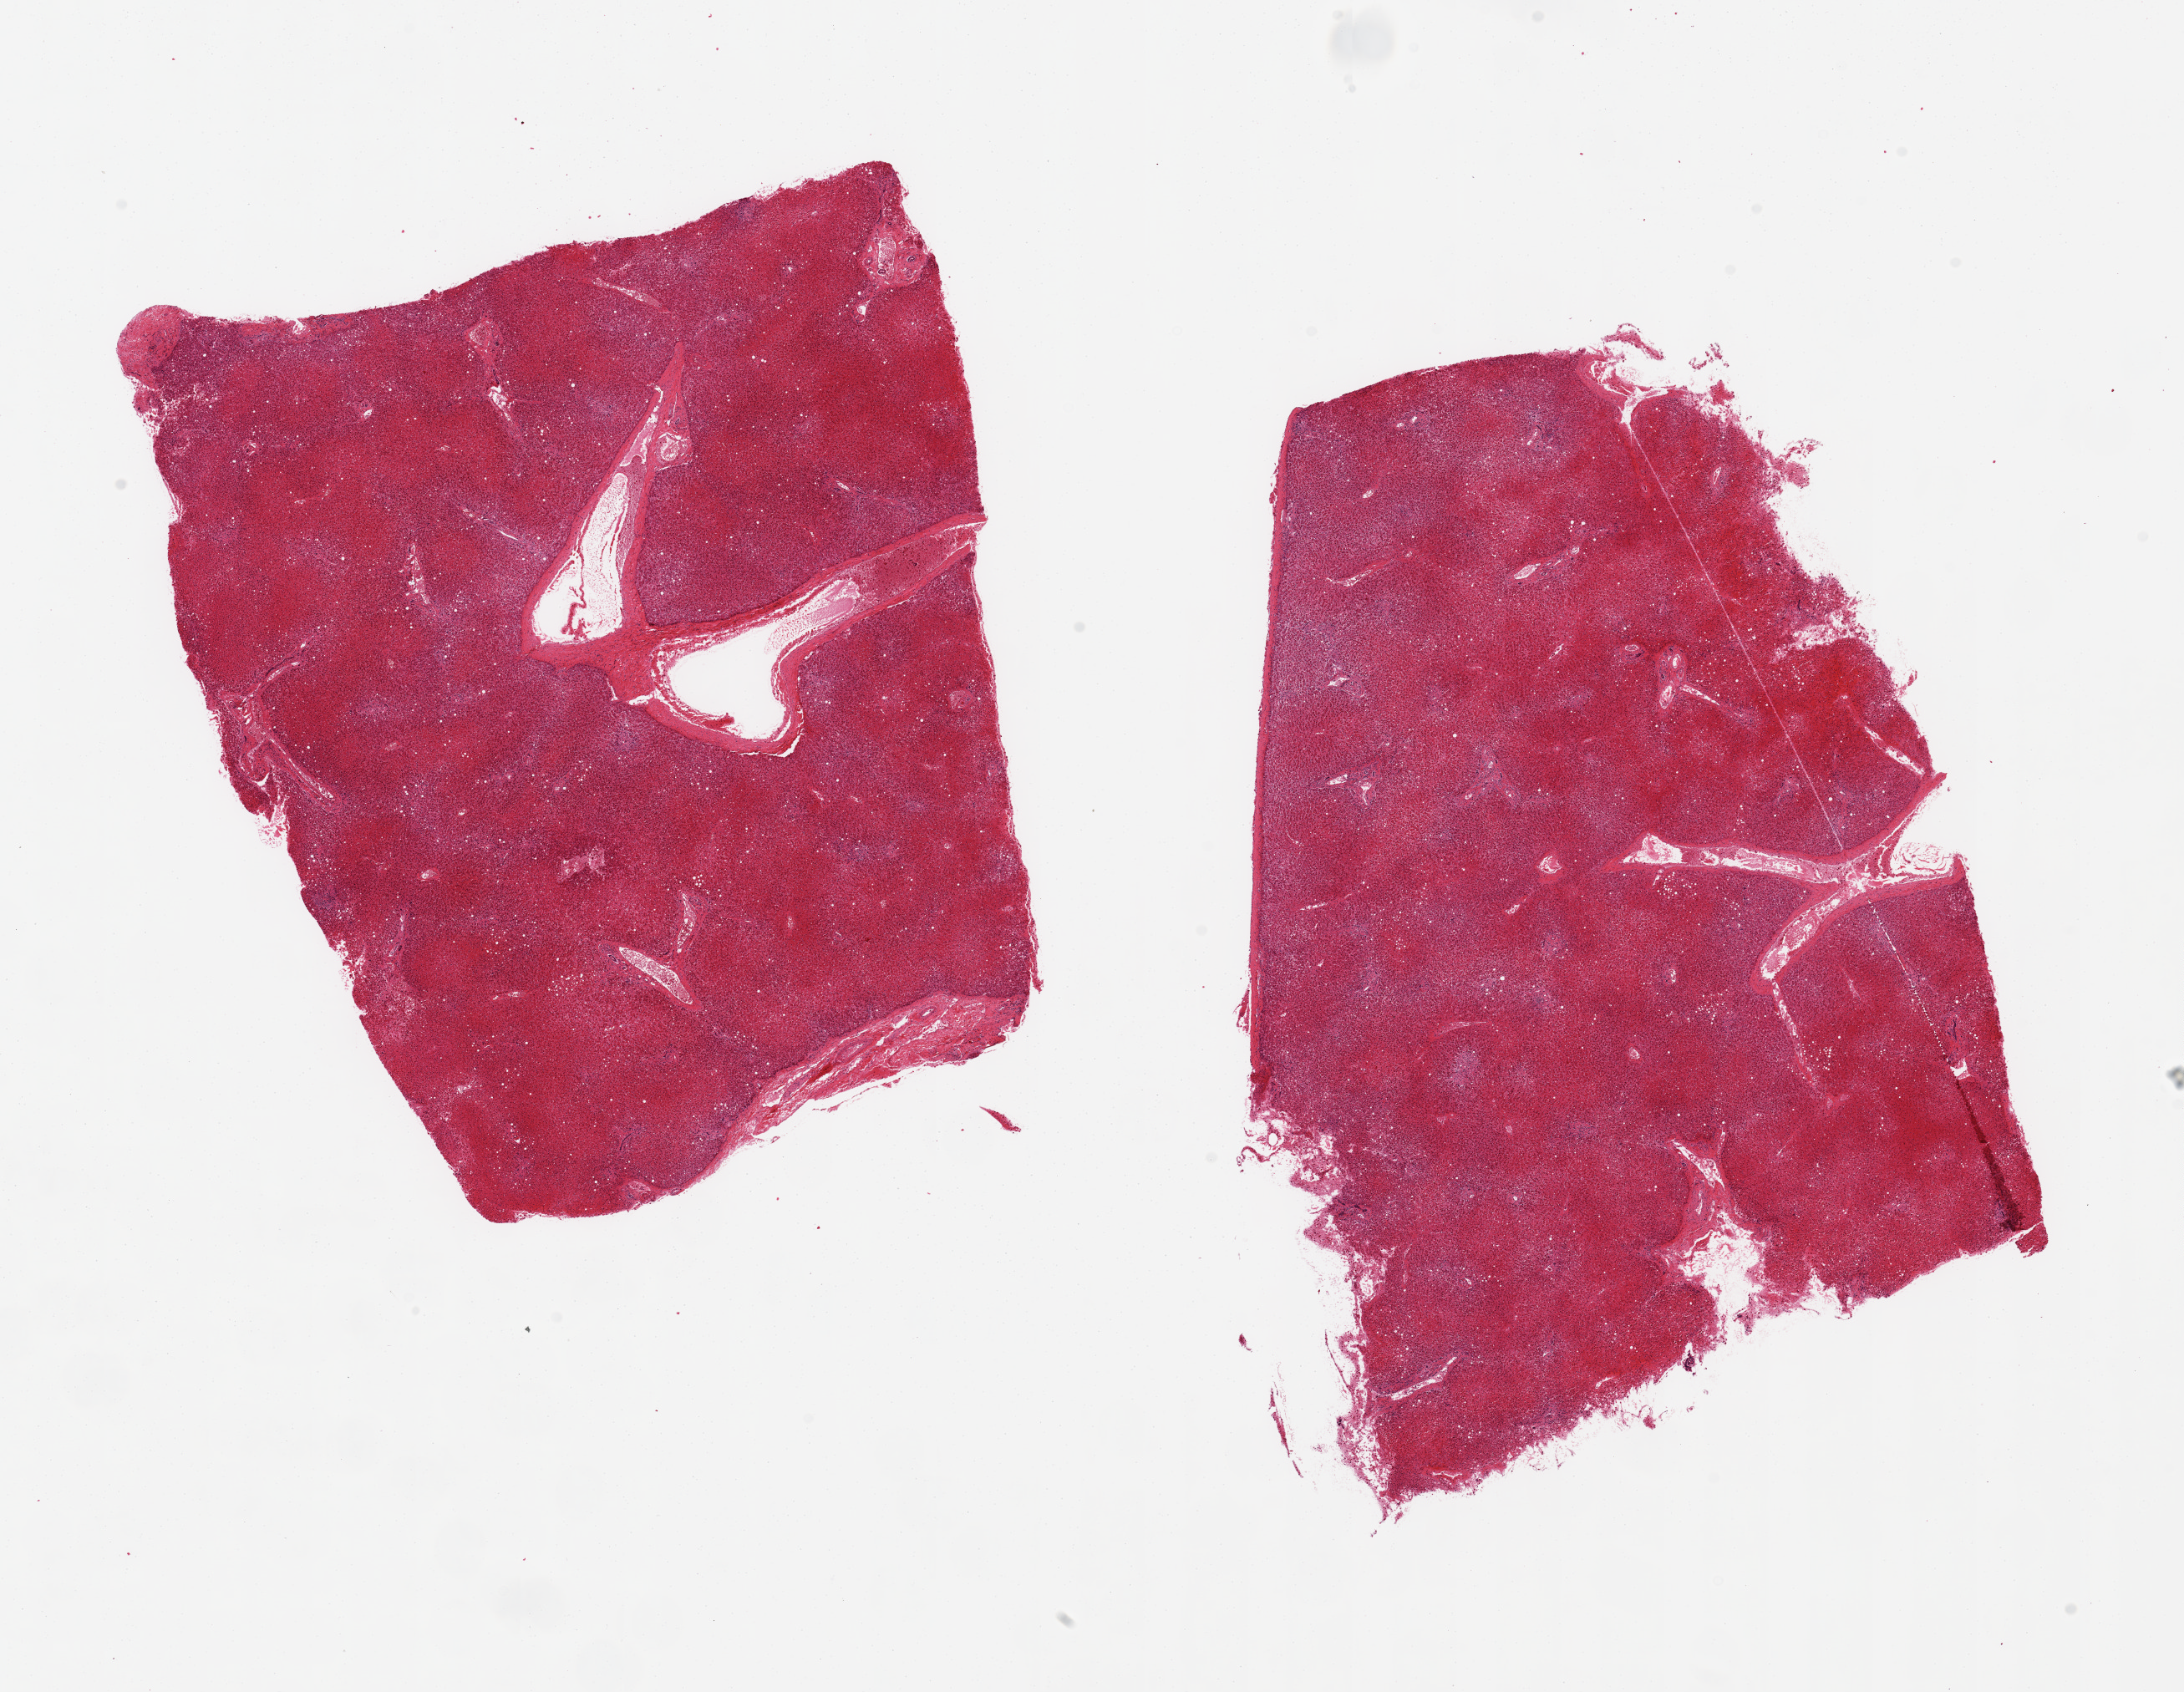
Digitized hematoxylin and eosin (H&E)-stained section, whole scanned area (about 20.7 x 16.0 mm, from a 20x scan) shown as a low-resolution overview. PAXgene-fixed, paraffin-embedded tissue. Sampled site (target tissue): liver. Tissue donor sample. Male donor.
Pathologist's review note for this sample: 2 pieces, 9x8 & 10x6mm; severe vascular congestion mainly centrolobular.